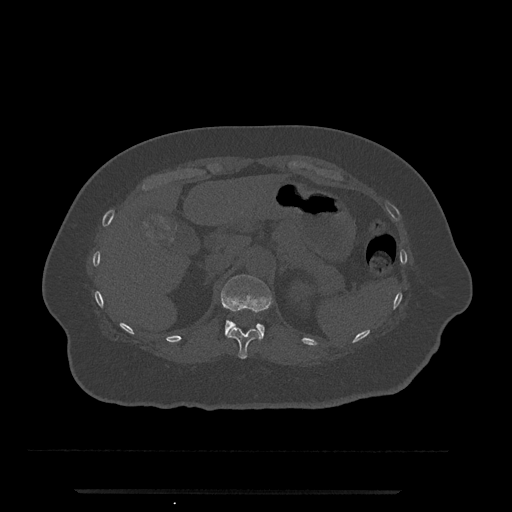
CT including the spine, one axial slice; slice 200 of 797 in the series (ordered by position); 120 kVp; bone window (W 1800 / L 400 HU); 0.5 mm slice thickness; 512 × 512 image matrix. Female patient, age 51 years. Case-level facts recorded for this patient, not image findings: primary cancer: neuro; vertebrae with lytic lesions (as recorded): T8.
Outlined on this slice (semi-automatically segmented with operator editing):
- T11 vertebra: box from (x=226, y=327) to (x=261, y=359) px
- T12 vertebra: (x=221, y=275)–(x=273, y=340)